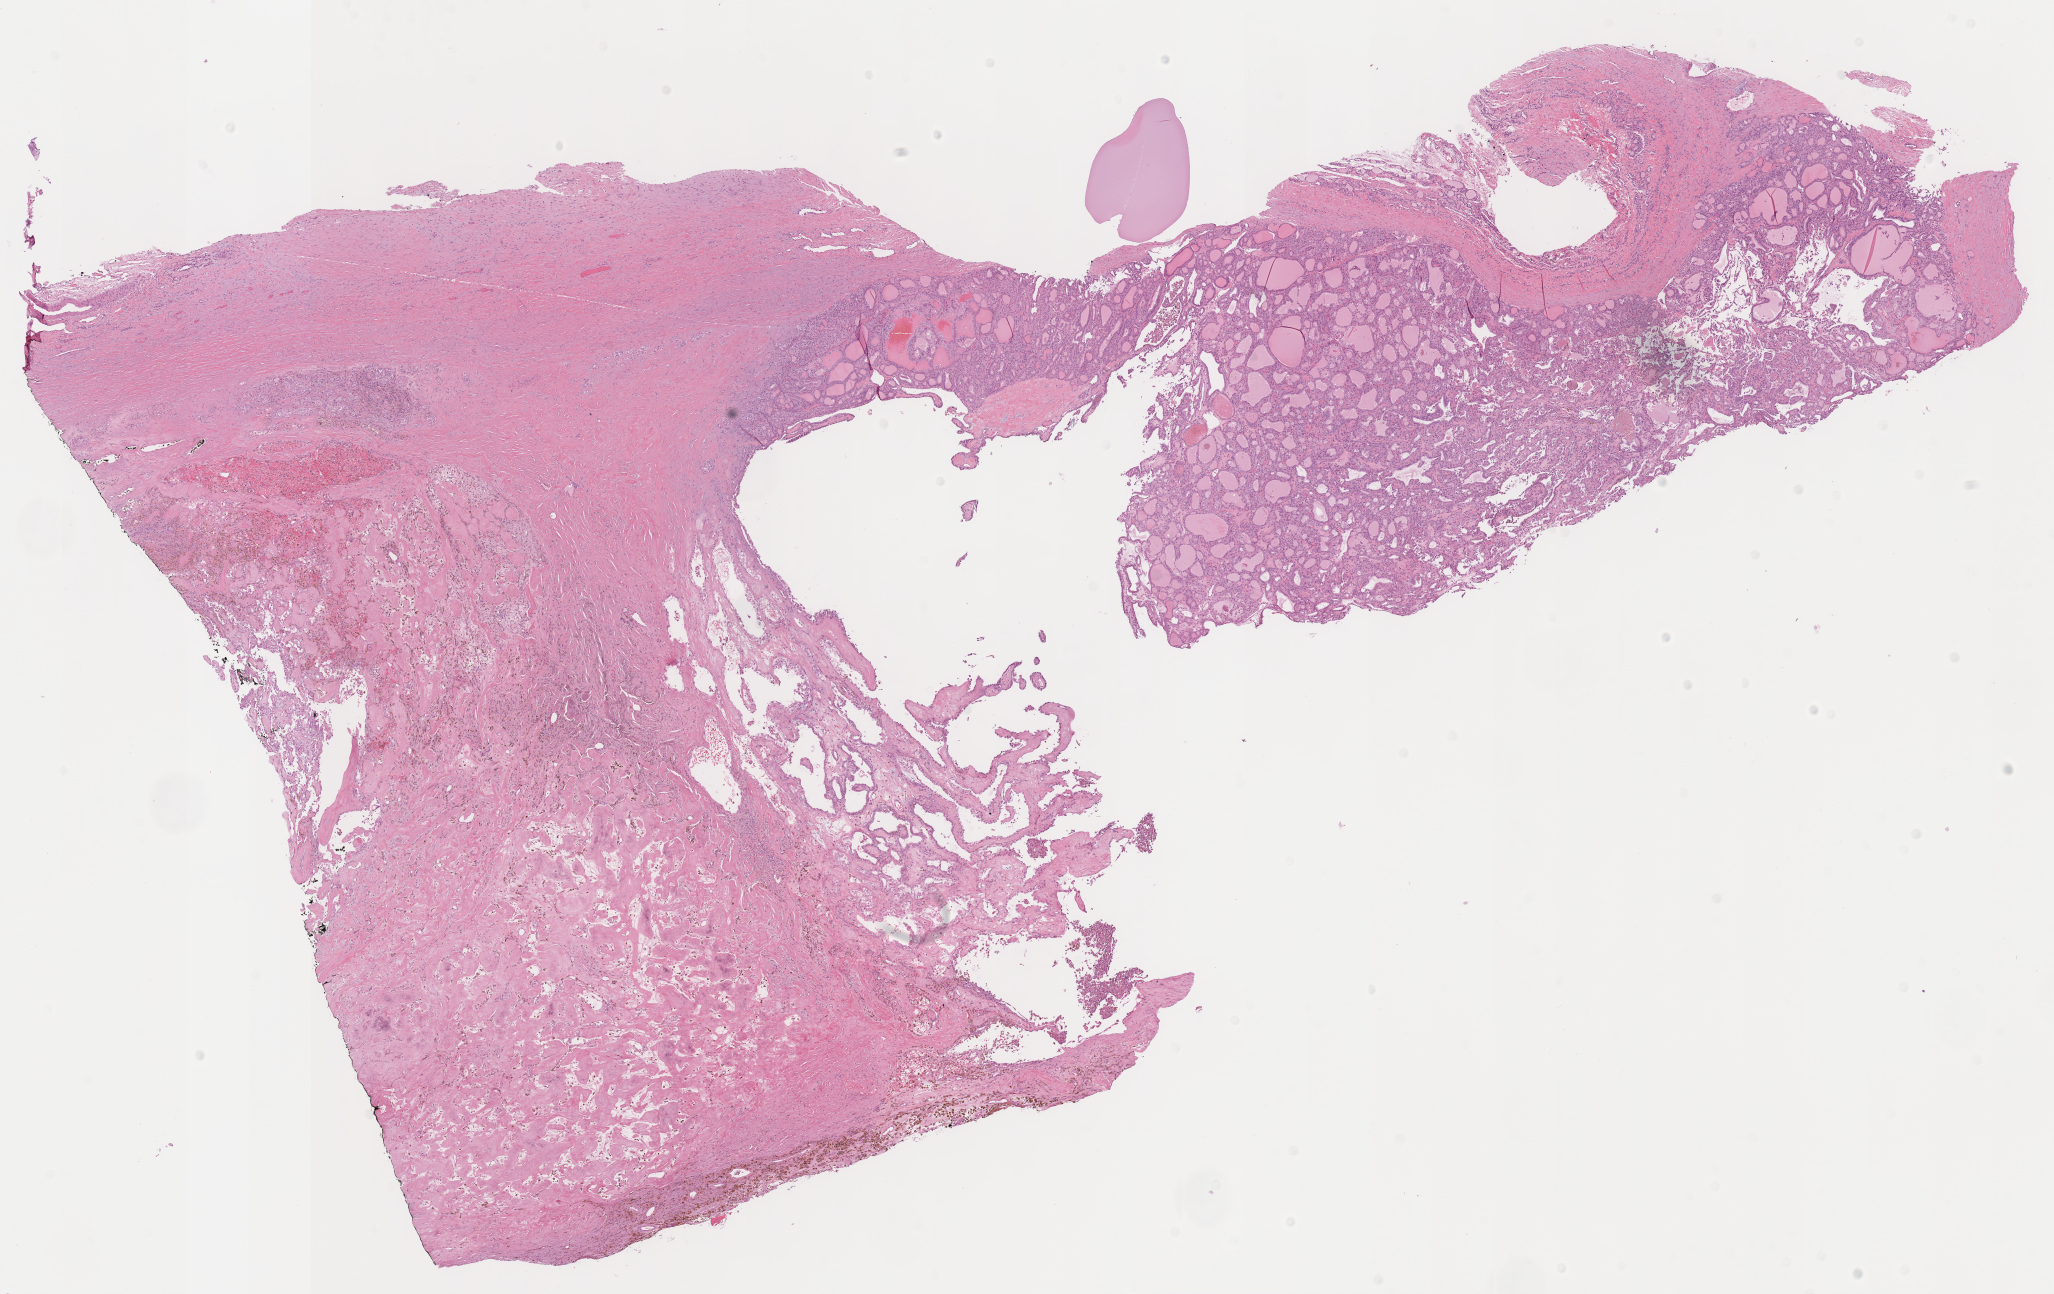
Whole-slide histology image, Hematoxylin and eosin (H&E) stained, shown as a low-resolution overview of the whole scanned area (about 16.2 x 10.2 mm, slide scanned at 40x), formalin-fixed paraffin-embedded (FFPE) diagnostic section, sample: primary tumour, thyroid. Male patient; age at initial diagnosis 76 years.
Pathologic diagnosis: Papillary carcinoma, follicular variant (thyroid gland).